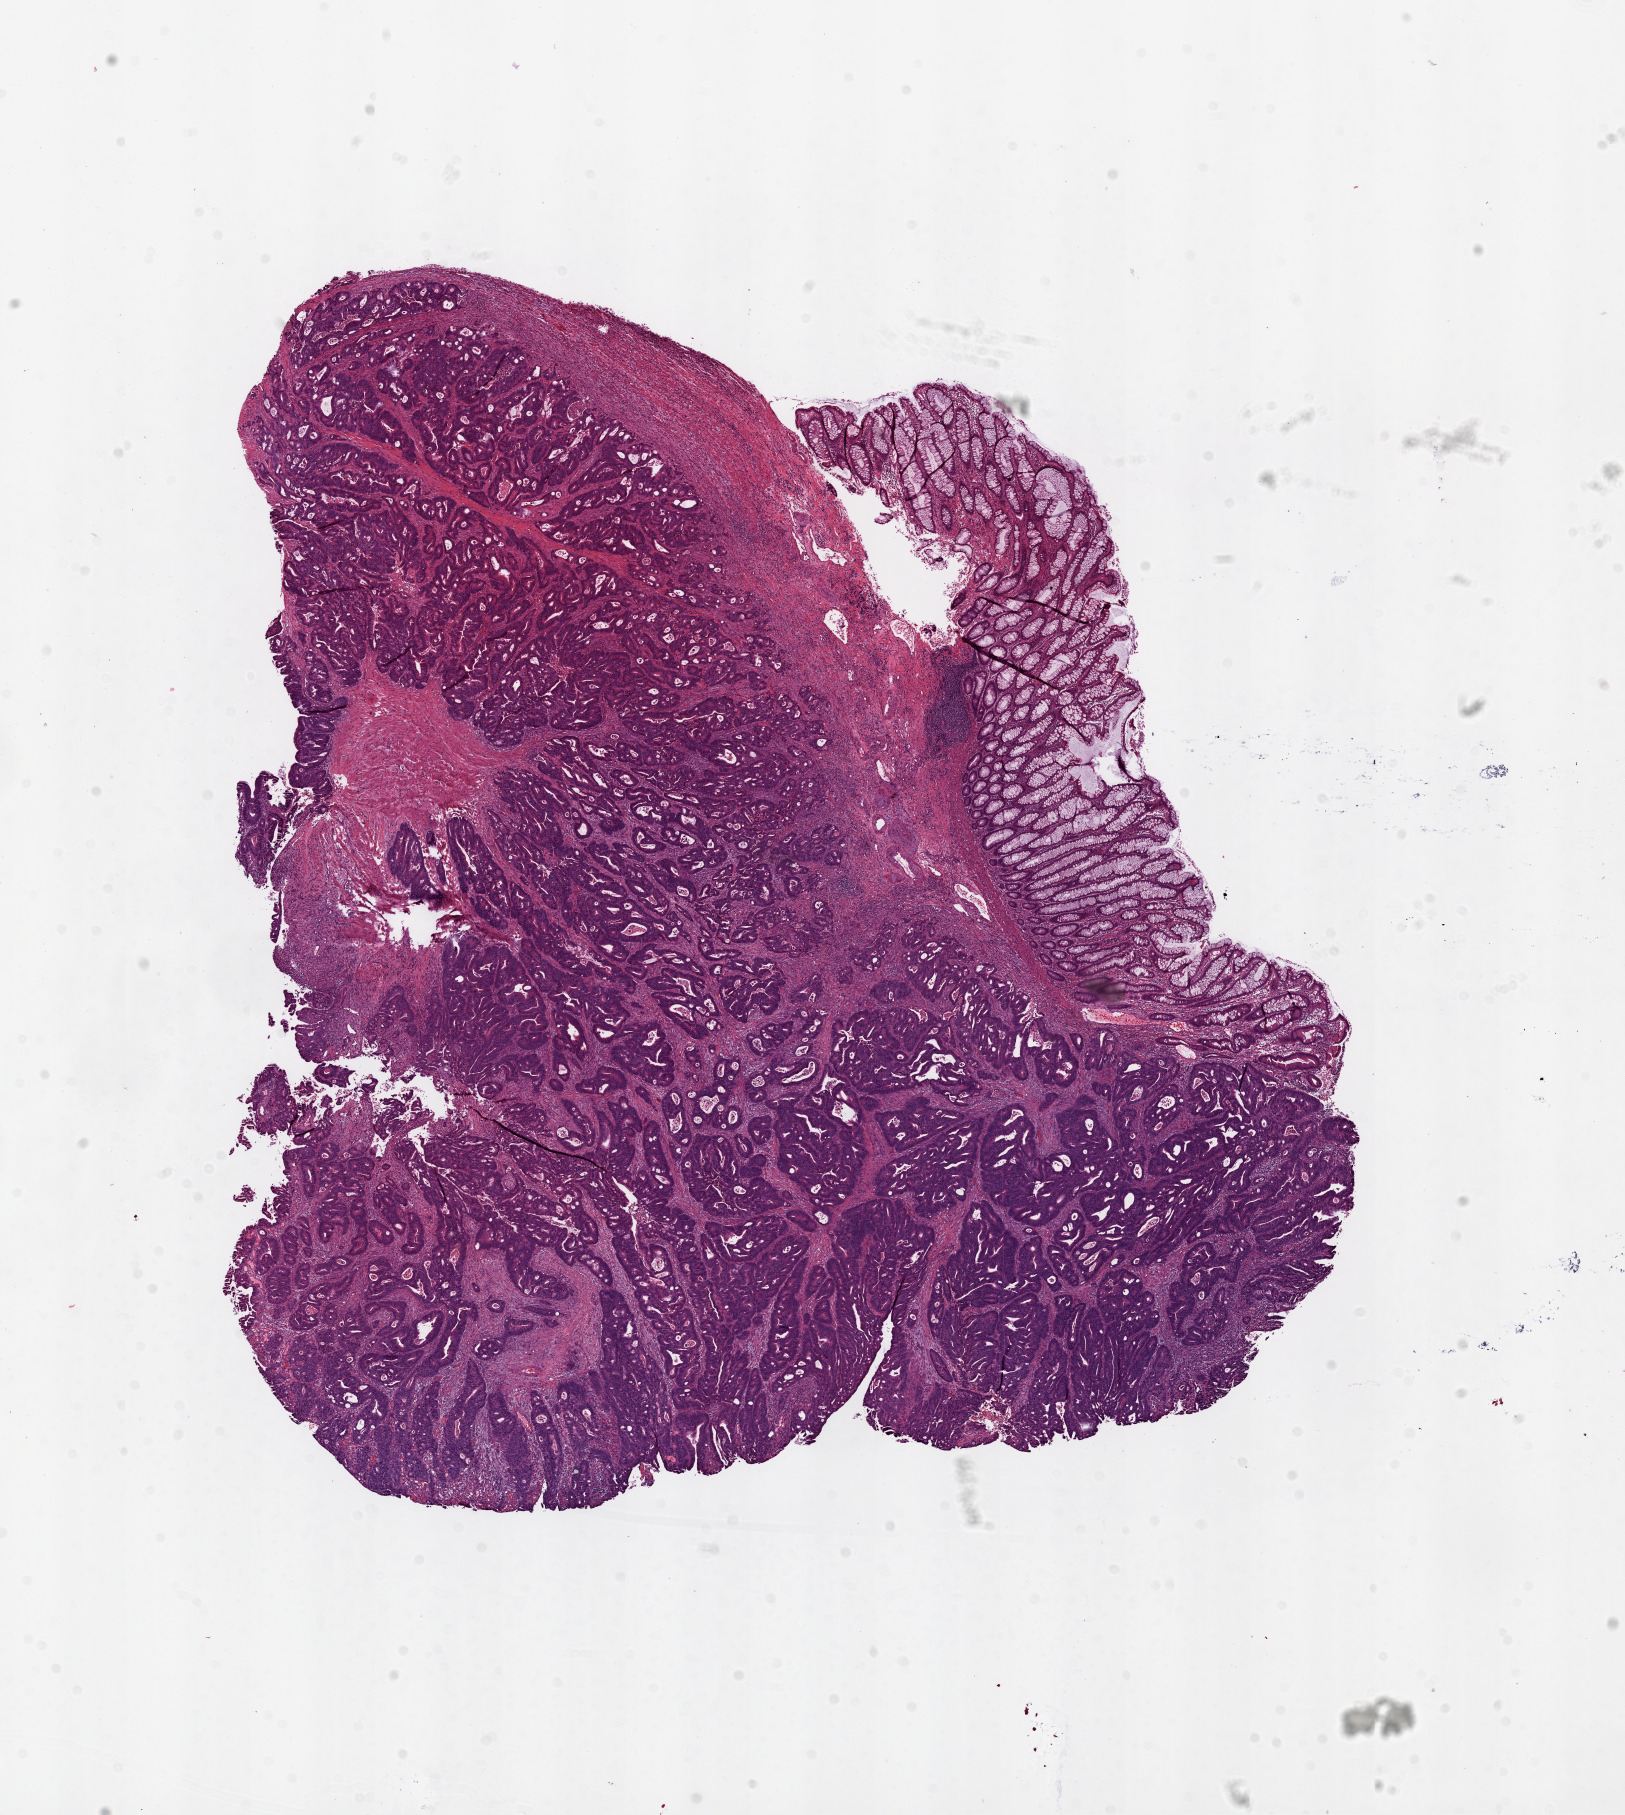
Whole-slide histology image, Hematoxylin and eosin (H&E) stained — a low-resolution overview of the entire scanned area, about 13.0 x 14.6 mm (from a 20x scan); frozen section from the top of the tissue portion; sample: primary tumour, colon. Female, age 72 years at initial diagnosis. Pathologist review of this section (percent, as recorded): tumour cells 76%, tumour nuclei 70%.
Diagnosis: Adenocarcinoma, NOS.